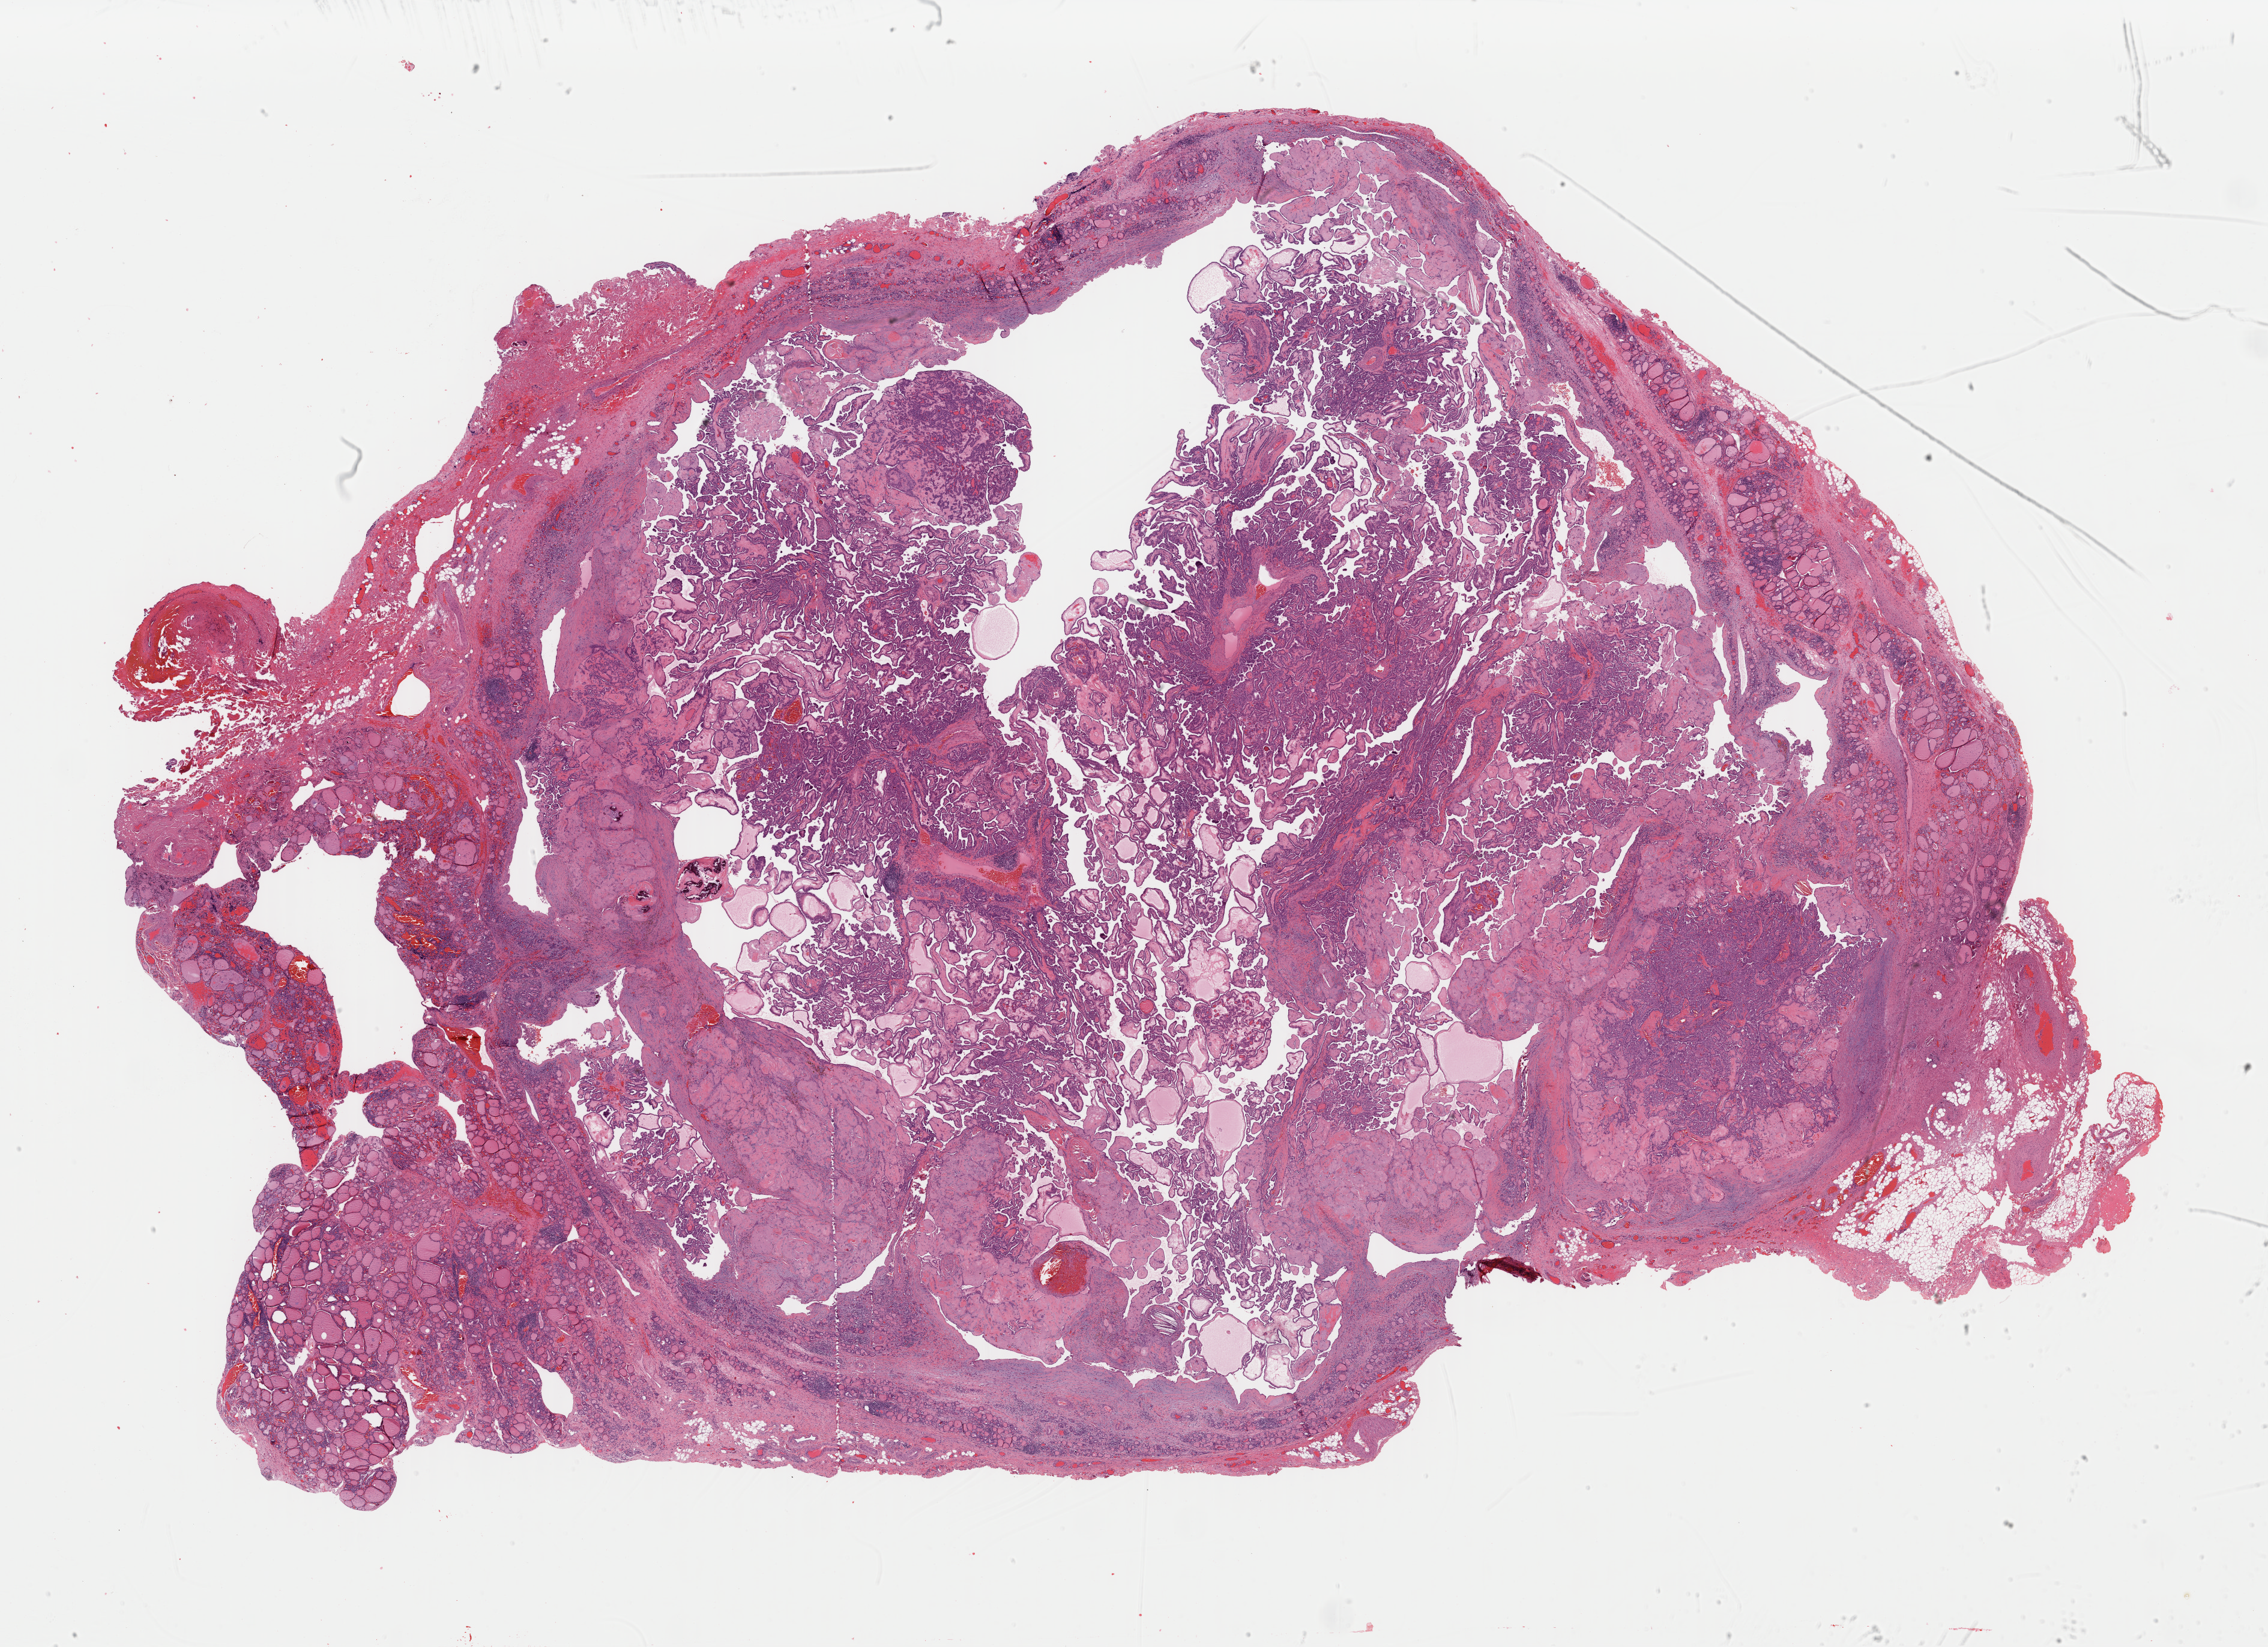
Hematoxylin and eosin (H&E) stained whole-slide image, a low-resolution overview of the entire scanned area, about 29.8 x 21.7 mm; formalin-fixed paraffin-embedded (FFPE) diagnostic section; primary tumour sample from the thyroid. Female, age 41 years at initial diagnosis.
Diagnosis: Papillary adenocarcinoma, NOS (thyroid gland).